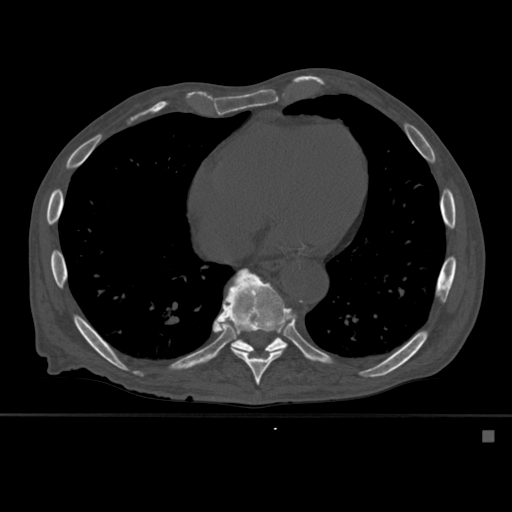
CT including the spine, one axial slice; bone window (W 1800 / L 400 HU); 1.5 mm slice thickness; 512 × 512 image matrix, field of view 373 × 373 mm. Patient: male, 78 years. Case-level facts recorded for this patient, not image findings: primary cancer: prostate.
Annotated regions visible in this slice (semi-automatically segmented with operator editing):
- T10 vertebra: box from (x=231, y=337) to (x=287, y=353) px
- T9 vertebra: (x=219, y=268)–(x=297, y=386)